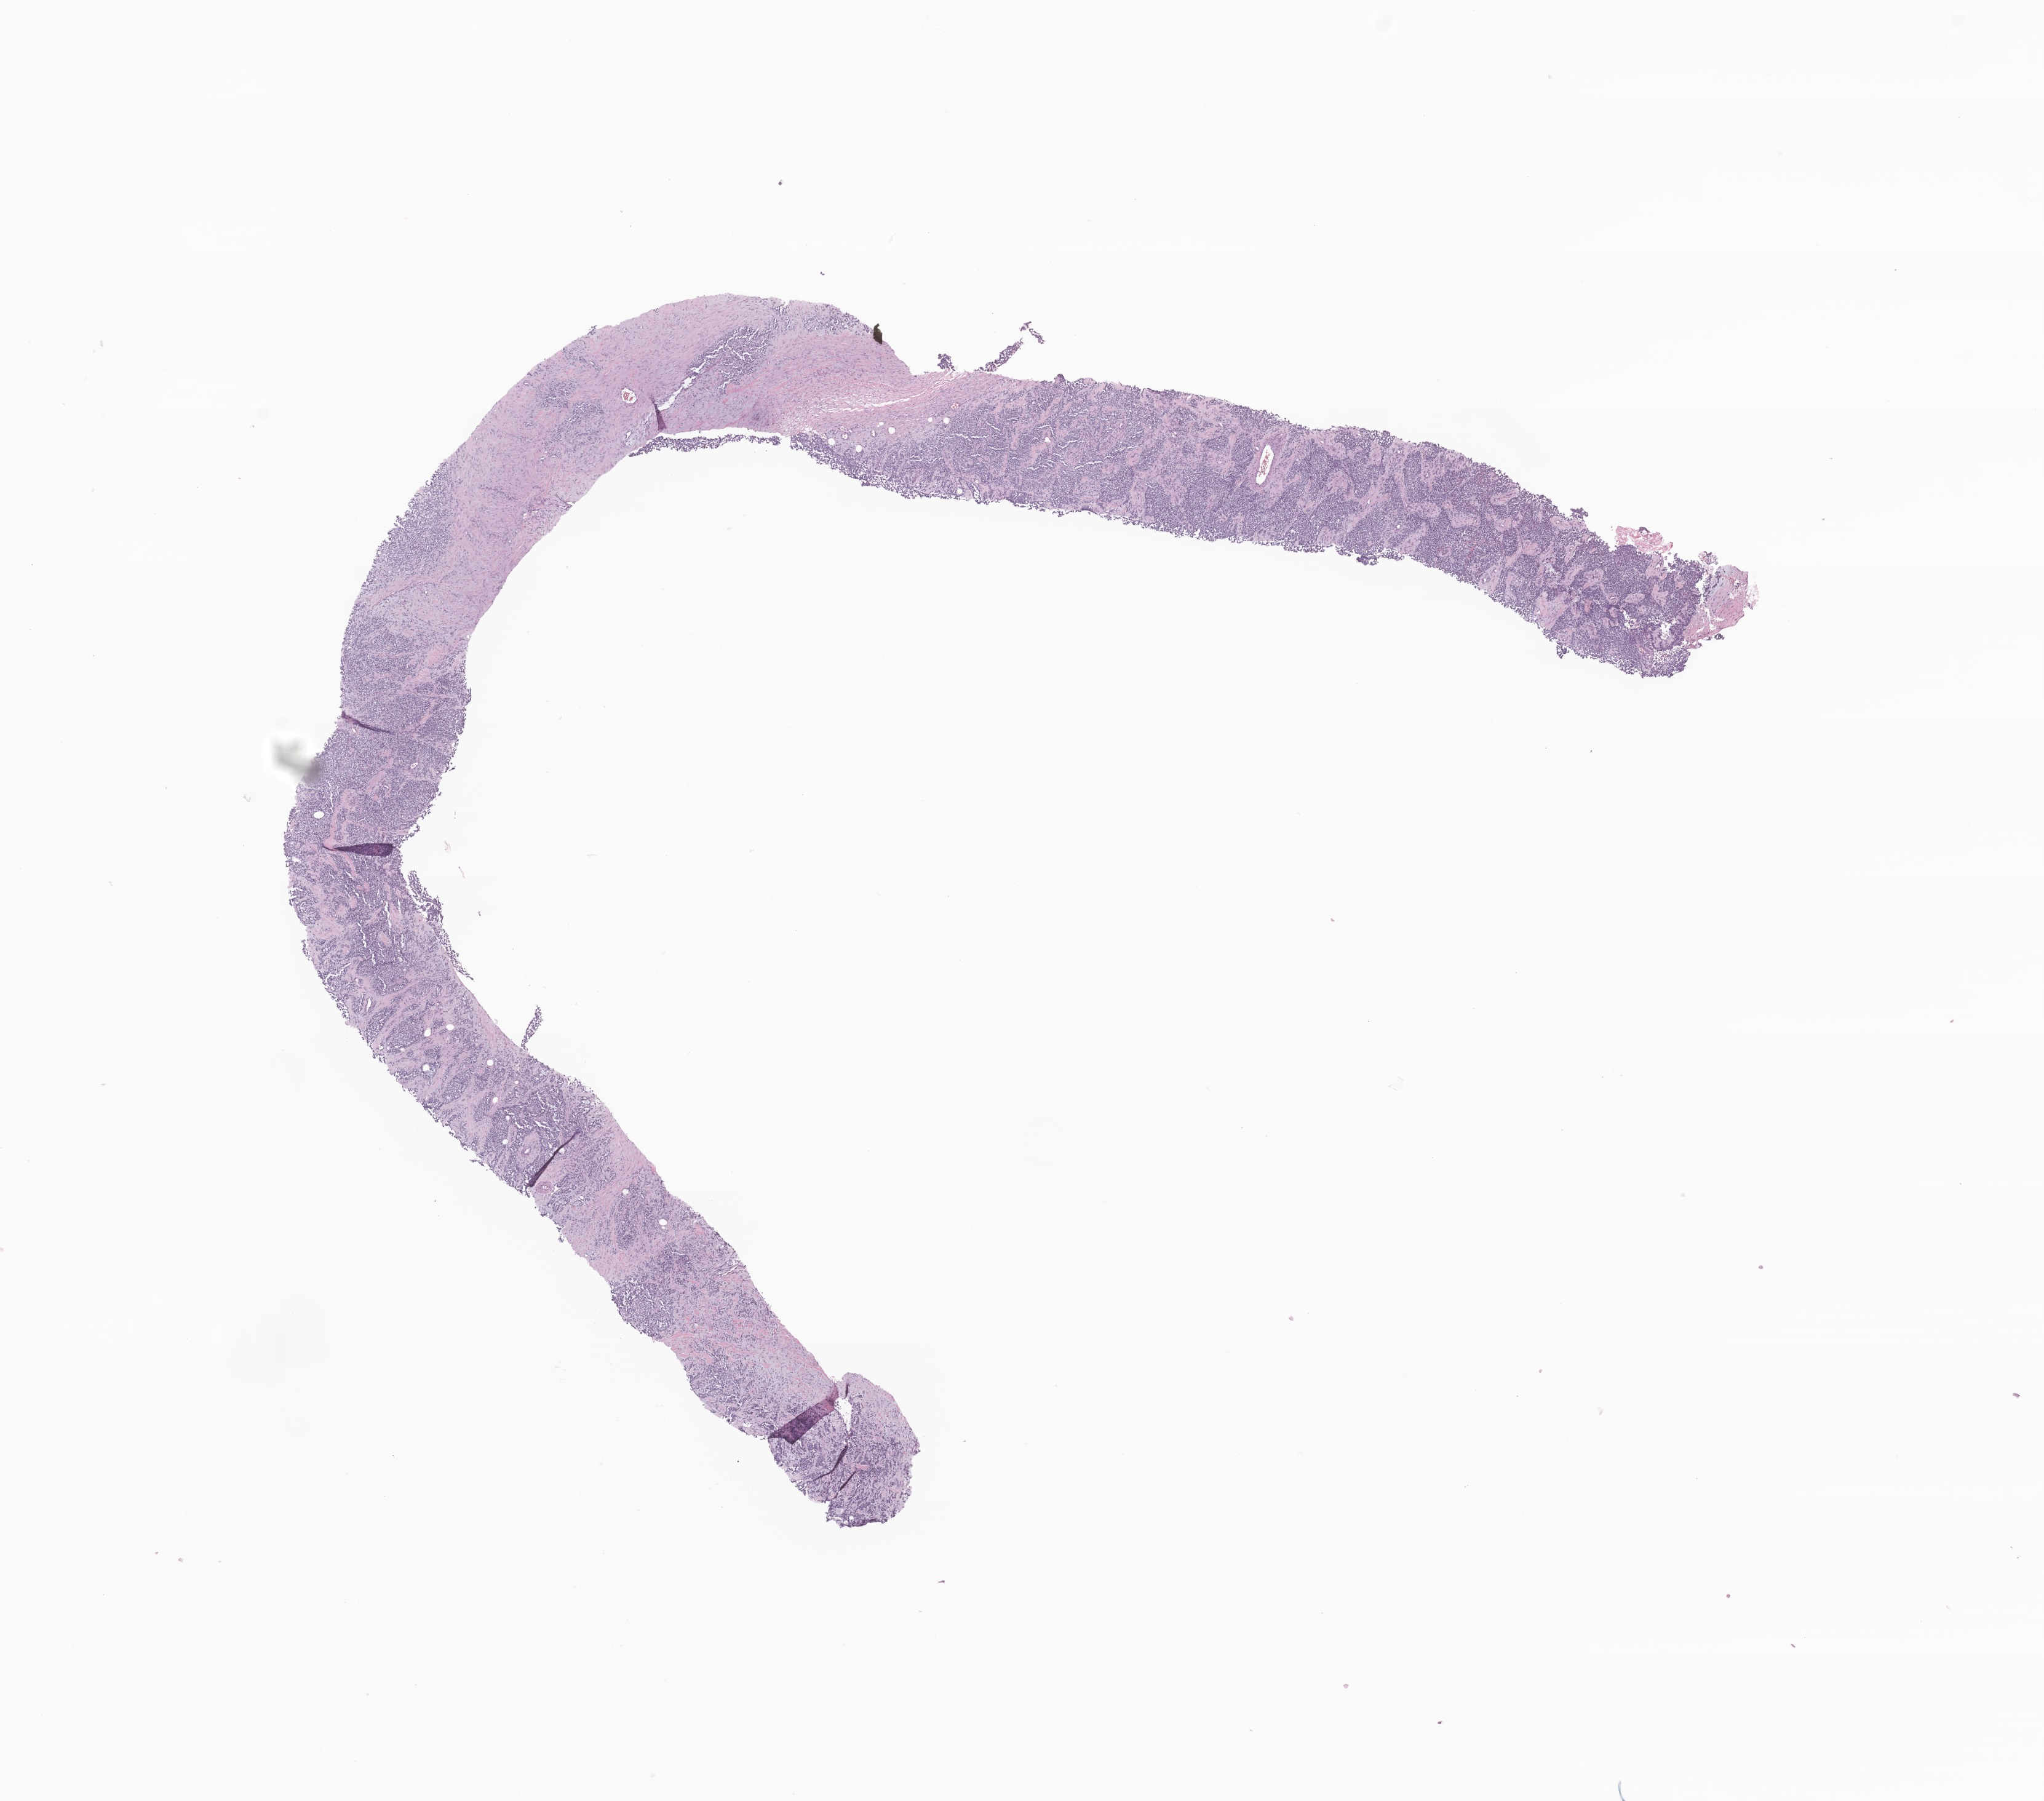
Haematoxylin and eosin whole-slide image of tumor tissue from the bone marrow, a low-resolution overview of the entire scanned area, about 14.0 x 12.3 mm; formalin-fixed, paraffin-embedded (FFPE) tissue. Male patient, age 188 months (15 years 8 months).
Diagnosis: Rhabdomyosarcoma, NOS.